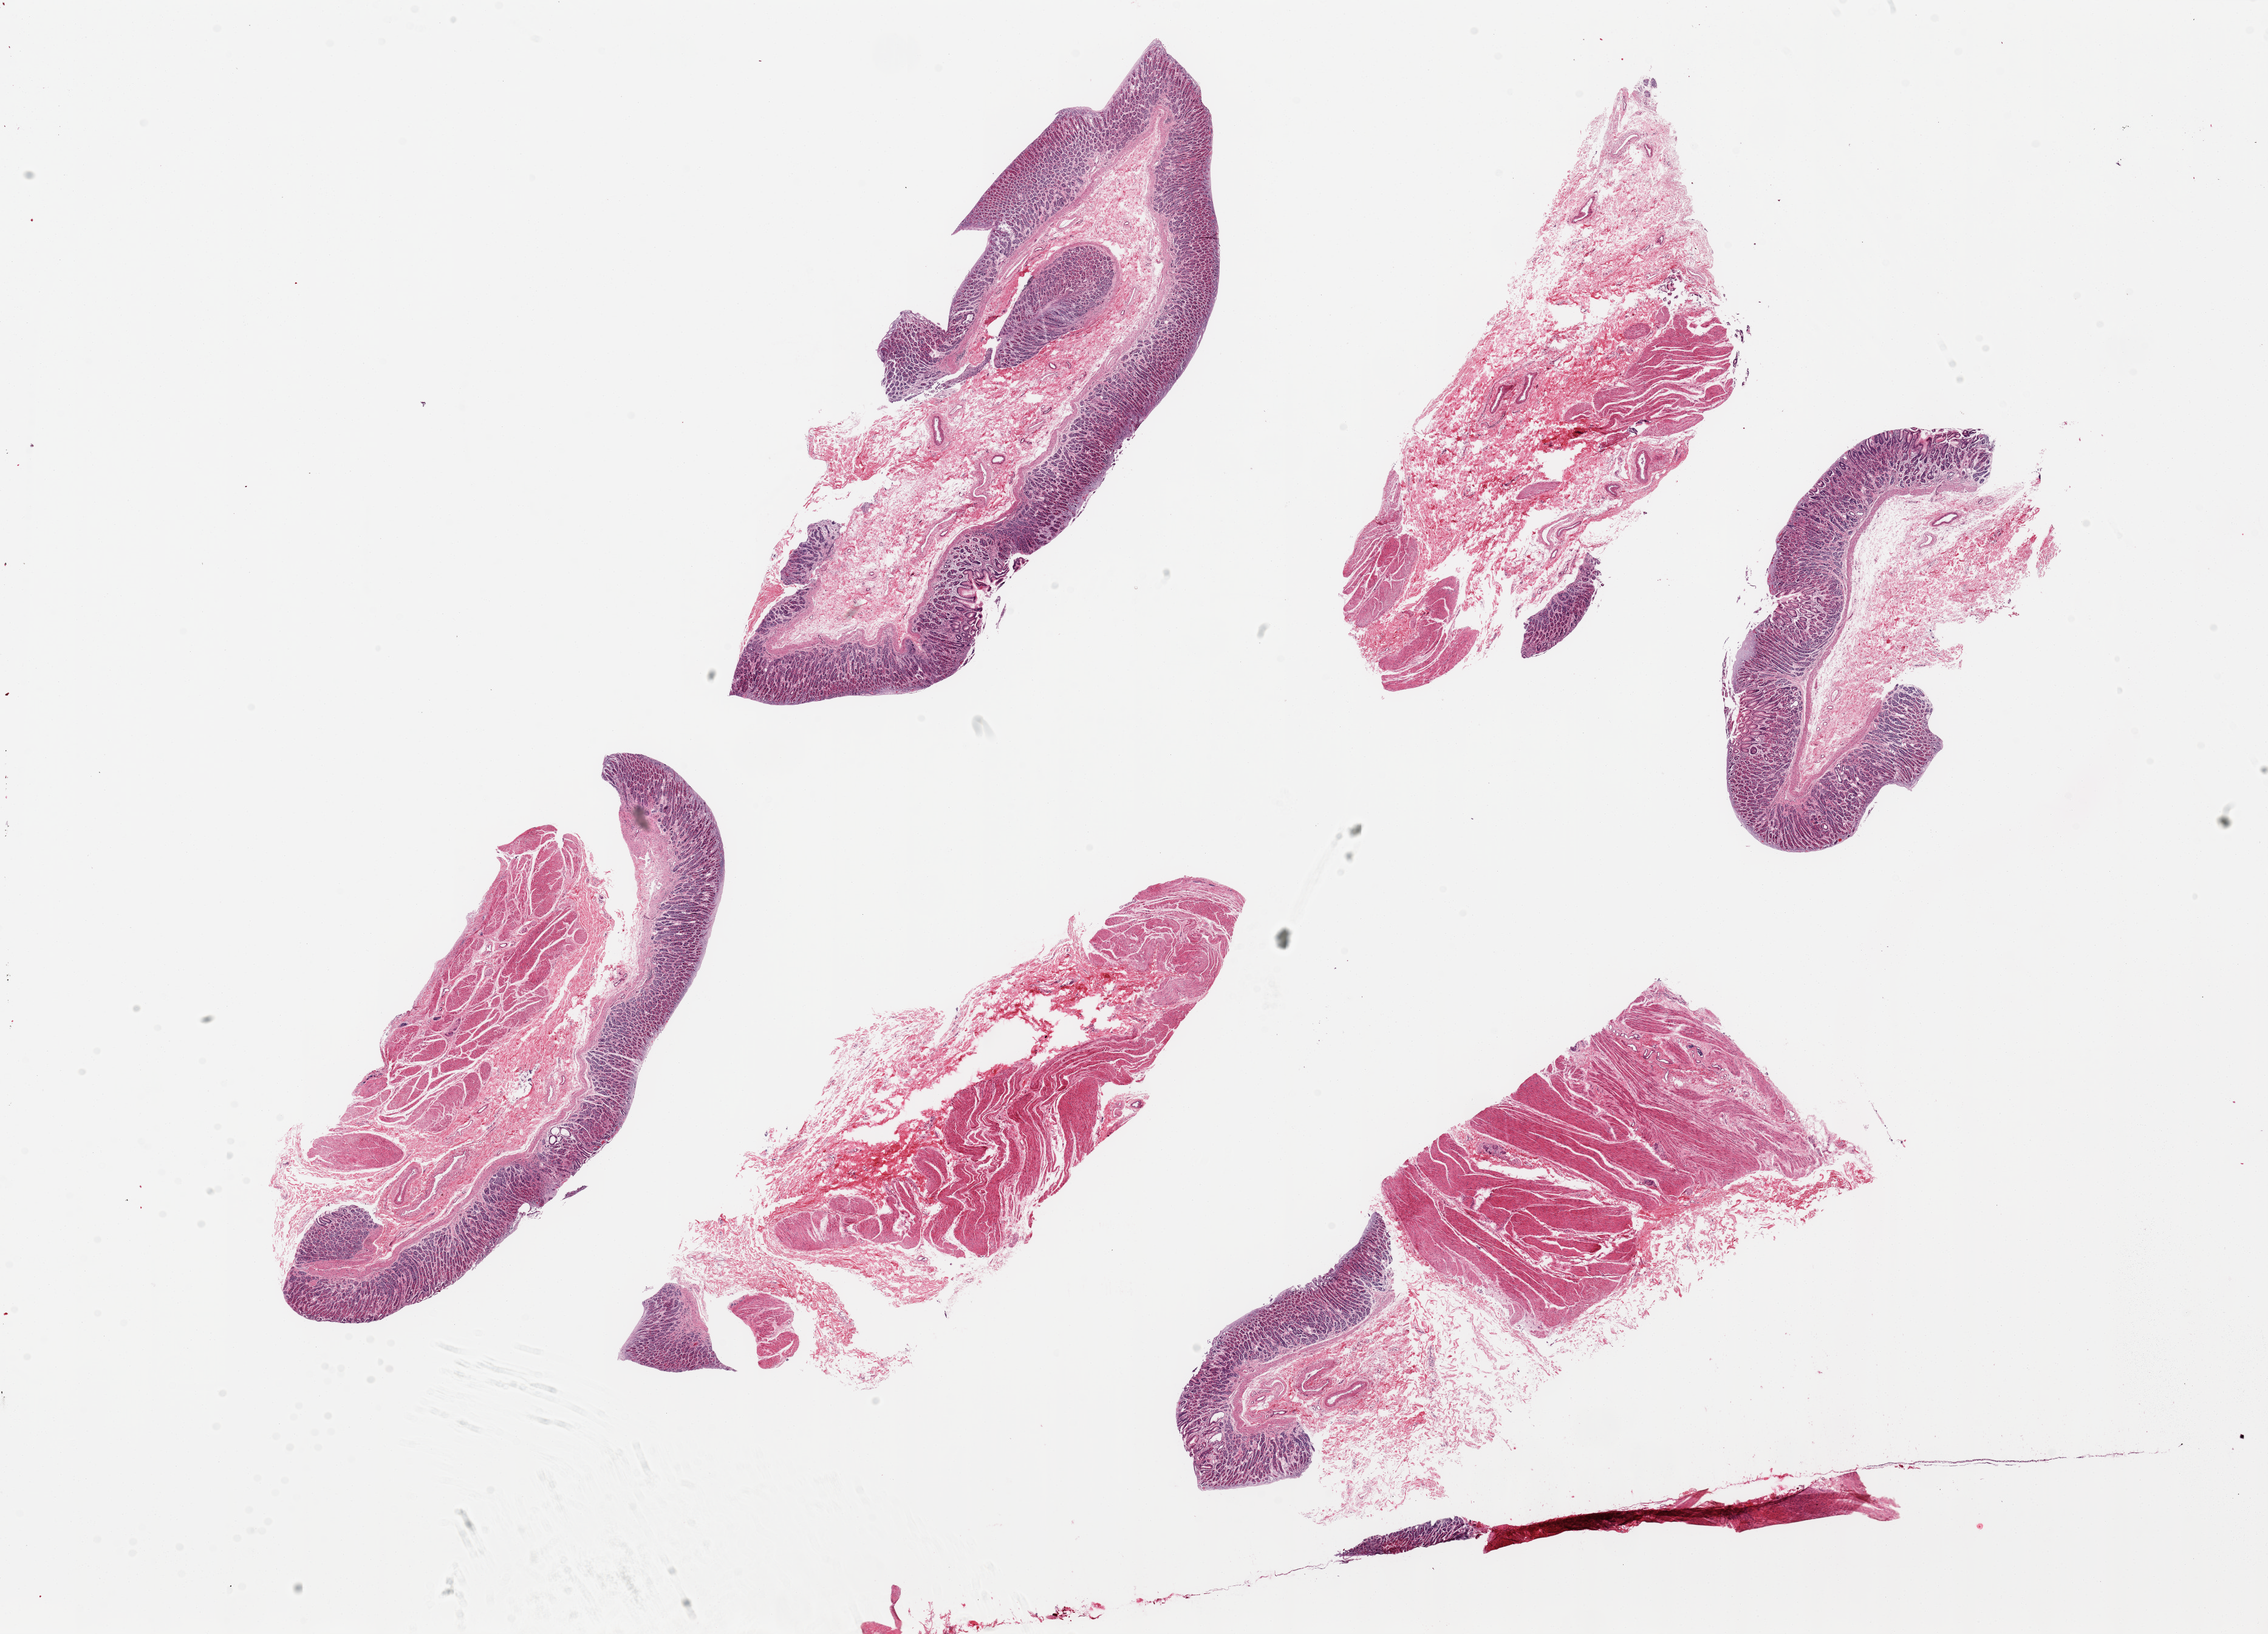
Digitized H&E-stained section, brightfield, shown as a low-resolution overview of the whole scanned area (about 29.5 x 21.3 mm, from a 20x scan); PAXgene-fixed, paraffin-embedded tissue; target tissue: stomach; donor tissue sample. Donor: male.
Review note (as recorded): 6 pieces, up to 10x3mm, mucosa 1 mm, well-preserved fundic mucosa except for foveolar.